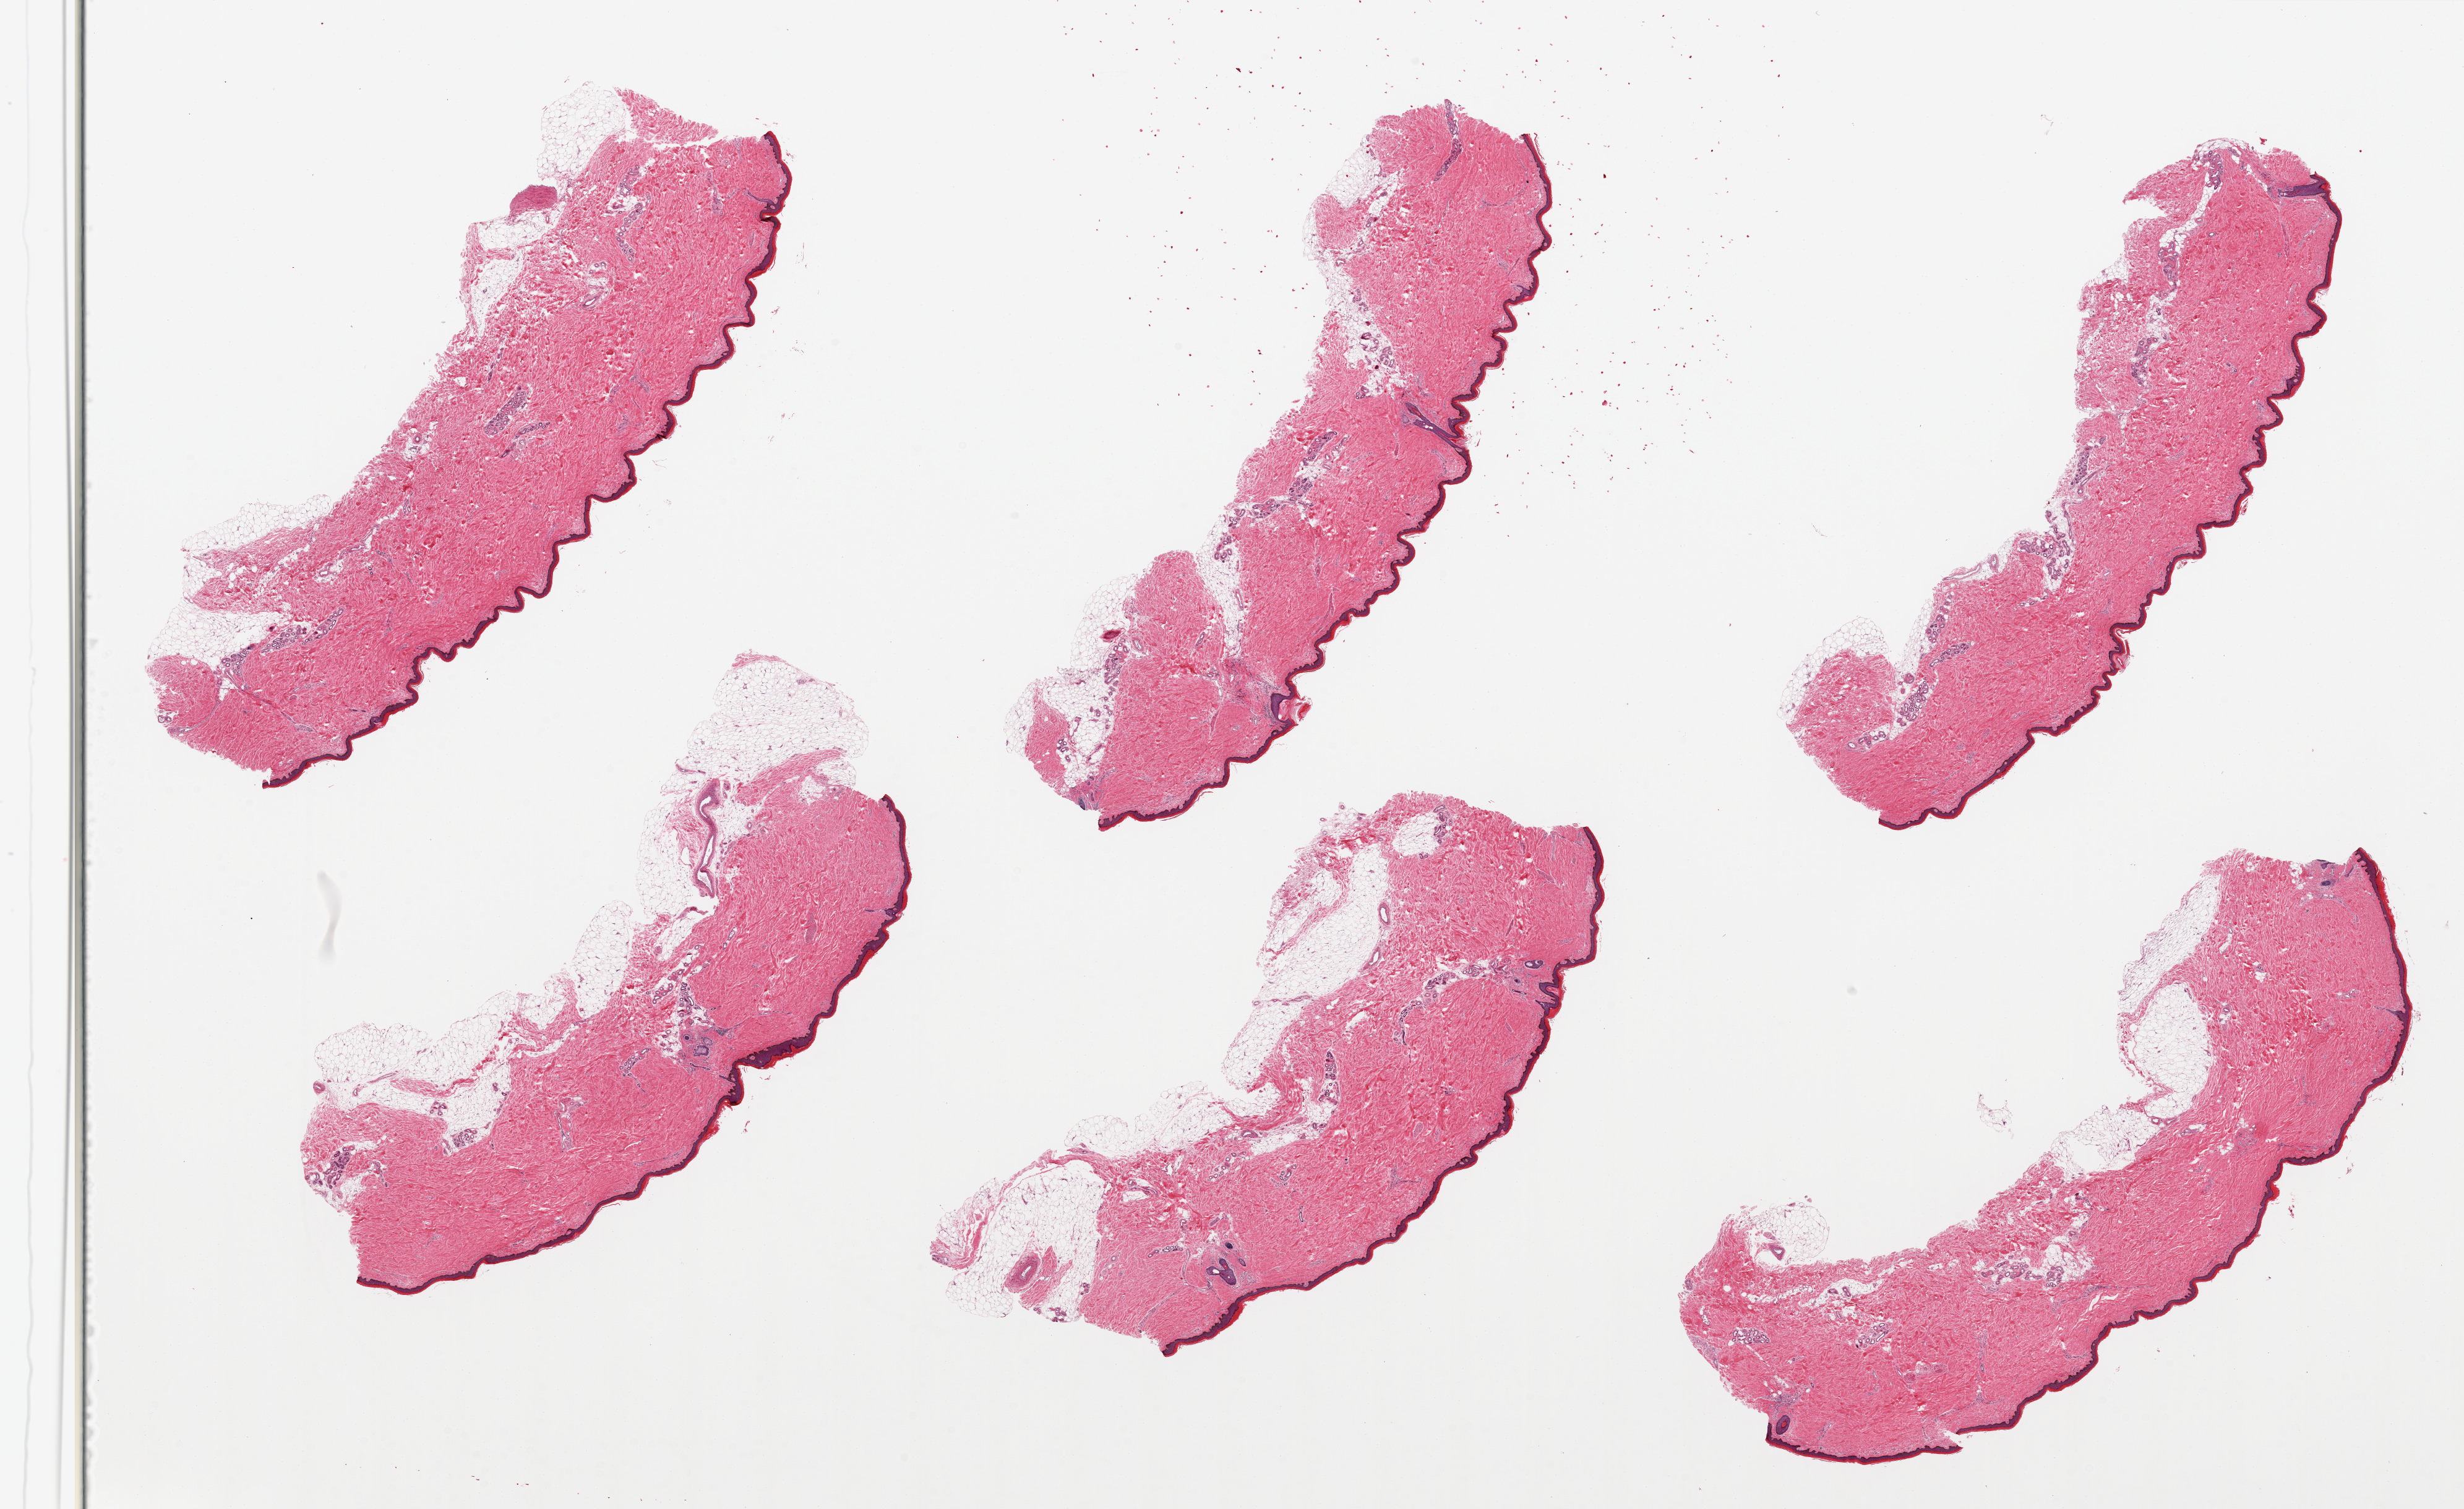
Digitized H&E-stained section, a low-resolution overview of the entire scanned area, about 31.5 x 19.3 mm. PAXgene-fixed paraffin-embedded (PFPE) section. Target tissue: skin of lower leg. Tissue donor sample.
• pathologist's review note for this sample: 6 pieces. 3 well trimmed; 3 with subcutaneous fat up to 1 mm